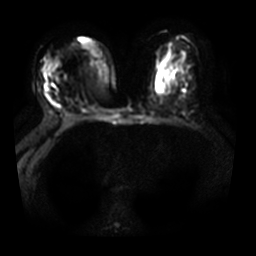
Breast MRI, one axial slice; slice 16 of 31 in the series (ordered by position); diffusion-weighted series; image 2 of 4 stored at this slice position (different b-values; order by instance number); 3 T; 5 mm slice thickness; 256 × 256 image matrix, field of view 350 × 350 mm. Female patient.
Annotated regions visible in this slice (manually delineated by an expert):
- tumour on diffusion-weighted imaging: bounding box <42,57,53,77> (left, top, right, bottom; pixels)